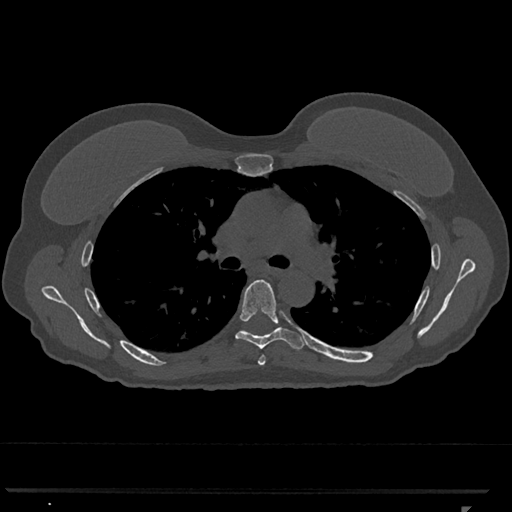
CT including the spine, one axial slice; position 763 of 793 along the scan axis; reconstruction kernel Br40s/3; bone window (W 1800 / L 400 HU); 512 × 512 image matrix. Female patient, age 62 years. From the clinical record (not read from this slice): primary cancer: renal.
Annotated regions visible in this slice (semi-automatically segmented with operator editing):
- T5 vertebra: box from (x=258, y=355) to (x=266, y=366) px
- T6 vertebra: (x=235, y=279)–(x=305, y=349)